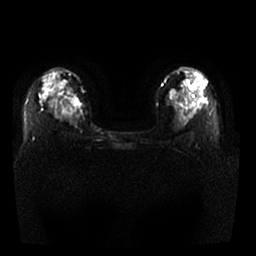
Breast MRI, one axial slice; position 21 of 29 along the scan axis; diffusion-weighted series; image 2 of 4 stored at this slice position (different b-values; order by instance number); 1.5 T; 256 × 256 image matrix, field of view 340 × 340 mm. Female patient.
Annotated regions visible in this slice (manually delineated by an expert):
- tumour on diffusion-weighted imaging: bounding box <69,97,79,108> (left, top, right, bottom; pixels)